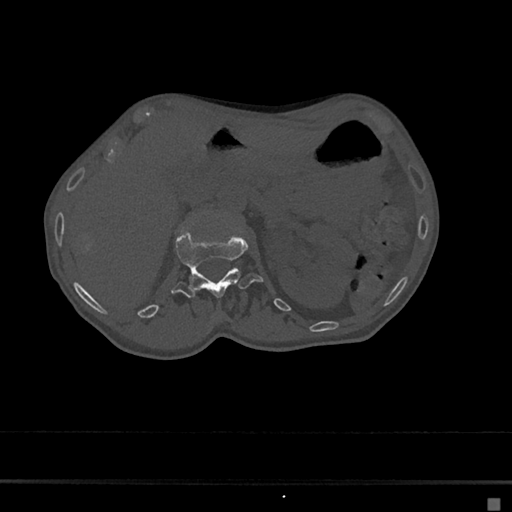
CT including the spine, one axial slice; slice 69 of 797 in the series (ordered by position); reconstruction kernel Br40s/3; 120 kVp; bone window (W 1800 / L 400 HU); 0.5 mm slice thickness; 512 × 512 image matrix. Female patient, age 68 years. Case-level facts recorded for this patient, not image findings: primary cancer: renal.
Structures marked on this image (semi-automatic segmentation, software-assisted and operator-edited):
- L1 vertebra: bounding box <172,228,263,299> (left, top, right, bottom; pixels)